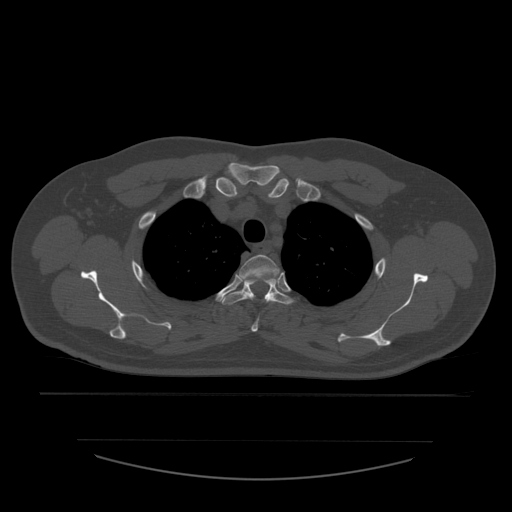
CT including the spine, one axial slice; position 440 of 532 along the scan axis; reconstruction kernel STANDARD; bone window (W 1800 / L 400 HU); 1.25 mm slice thickness; 512 × 512 image matrix, field of view 441 × 441 mm. Patient age 44 years. Case-level facts recorded for this patient, not image findings: primary cancer: soft tissue sarcoma.
Outlined on this slice (semi-automatically segmented with operator editing):
- T2 vertebra: box from (x=240, y=255) to (x=280, y=332) px
- T3 vertebra: (x=219, y=277)–(x=293, y=305)